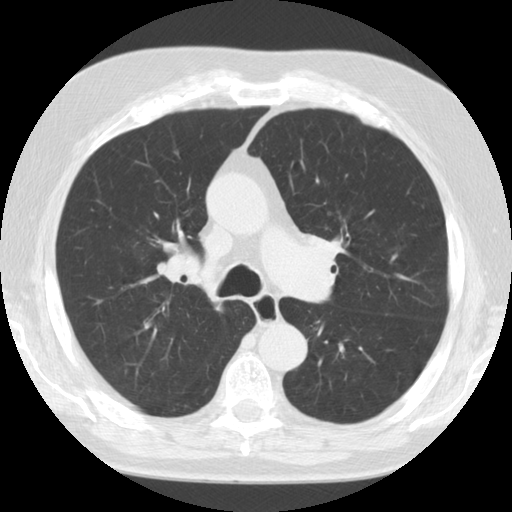
Axial slice from a low-dose chest CT screening exam; first (baseline) screen; lung window (W 1500 / L -600 HU); 512 × 512 image matrix. Male, age 72 years at enrolment. Former smoker at enrolment.
Expert-annotated lung lesion, bounding box <135,231,214,296> (left, top, right, bottom; pixels). Screening reader's record for this exam: no non-calcified nodule ≥4 mm recorded.